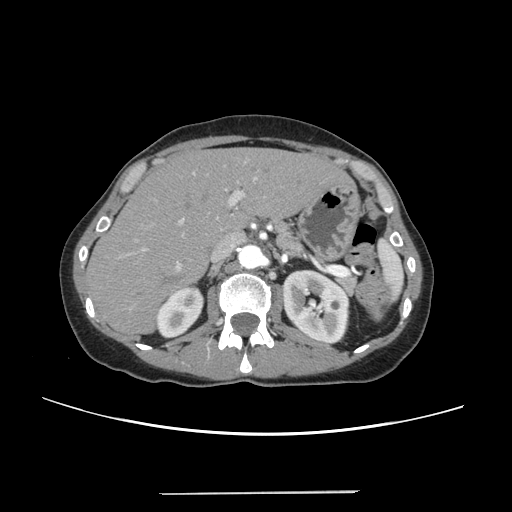
Contrast-enhanced abdominal CT, one axial slice. Position 158 of 240 along the scan axis. Intravenous contrast given. Soft-tissue window (W 400 / L 40 HU). 1.25 mm slice thickness. 512 × 512 image matrix. Female patient, age 60 years. Case-level facts recorded for this patient, not image findings: diagnosis: colorectal cancer liver metastases, imaged before liver resection; multiple liver metastases: no; largest metastasis: 1.5 cm; chemotherapy before resection: yes.
Structures marked on this image (manually delineated by an expert):
- liver: box from (x=88, y=148) to (x=348, y=333) px
- planned liver remnant (the part of the liver to remain after resection): (x=88, y=148)–(x=346, y=333)
- portal vein (with intrahepatic branches): (x=126, y=171)–(x=258, y=270)